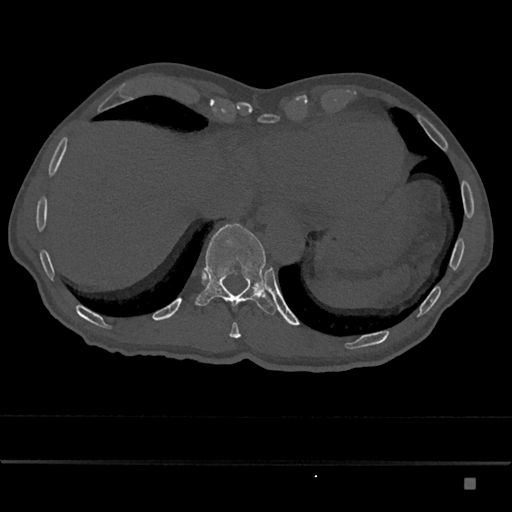
CT including the spine, one axial slice. Slice 689 of 797 in the series (ordered by position). Bone window (W 1800 / L 400 HU). 0.5 mm slice thickness. 512 × 512 image matrix, field of view 390 × 390 mm. Male patient, age 72 years. From the clinical record (not read from this slice): primary cancer: prostate.
Outlined on this slice (semi-automatic segmentation, software-assisted and operator-edited):
- T10 vertebra: bounding box [x1, y1, x2, y2] px = [229, 323, 241, 338]
- T11 vertebra: [194, 223, 276, 315]